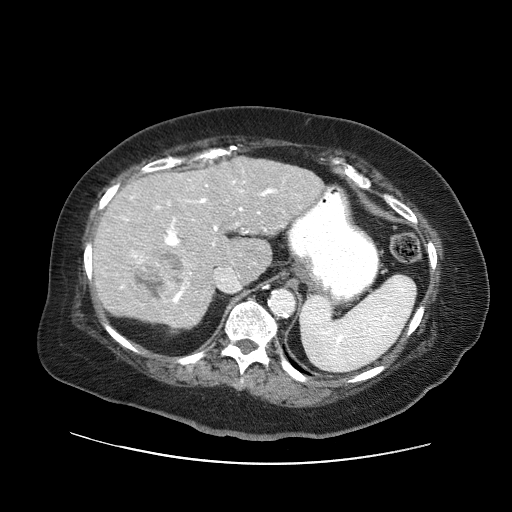
Contrast-enhanced abdominal CT (liver protocol), one axial slice. Position 37 of 71 along the scan axis. Reconstruction kernel STANDARD. Soft-tissue window (W 400 / L 40 HU). 2.5 mm slice thickness. 512 × 512 image matrix. From the clinical record (not read from this slice): diagnosis: hepatocellular carcinoma (patient treated with transarterial chemoembolisation; whether this scan precedes or follows treatment is not stated here); TNM stage (as recorded): Stage-II; Child-Pugh class: A; tumour differentiation: poorly differentiated; tumour nodularity: multinodular.
Annotated regions visible in this slice (semi-automatic segmentation, software-assisted and operator-edited):
- liver parenchyma outside the tumour (the mass and vessels are separate outlines, so this box may not span the whole liver): bounding box <92,156,322,328> (left, top, right, bottom; pixels)
- mass: <135,247,187,300>
- liver vessels: <120,171,283,304>